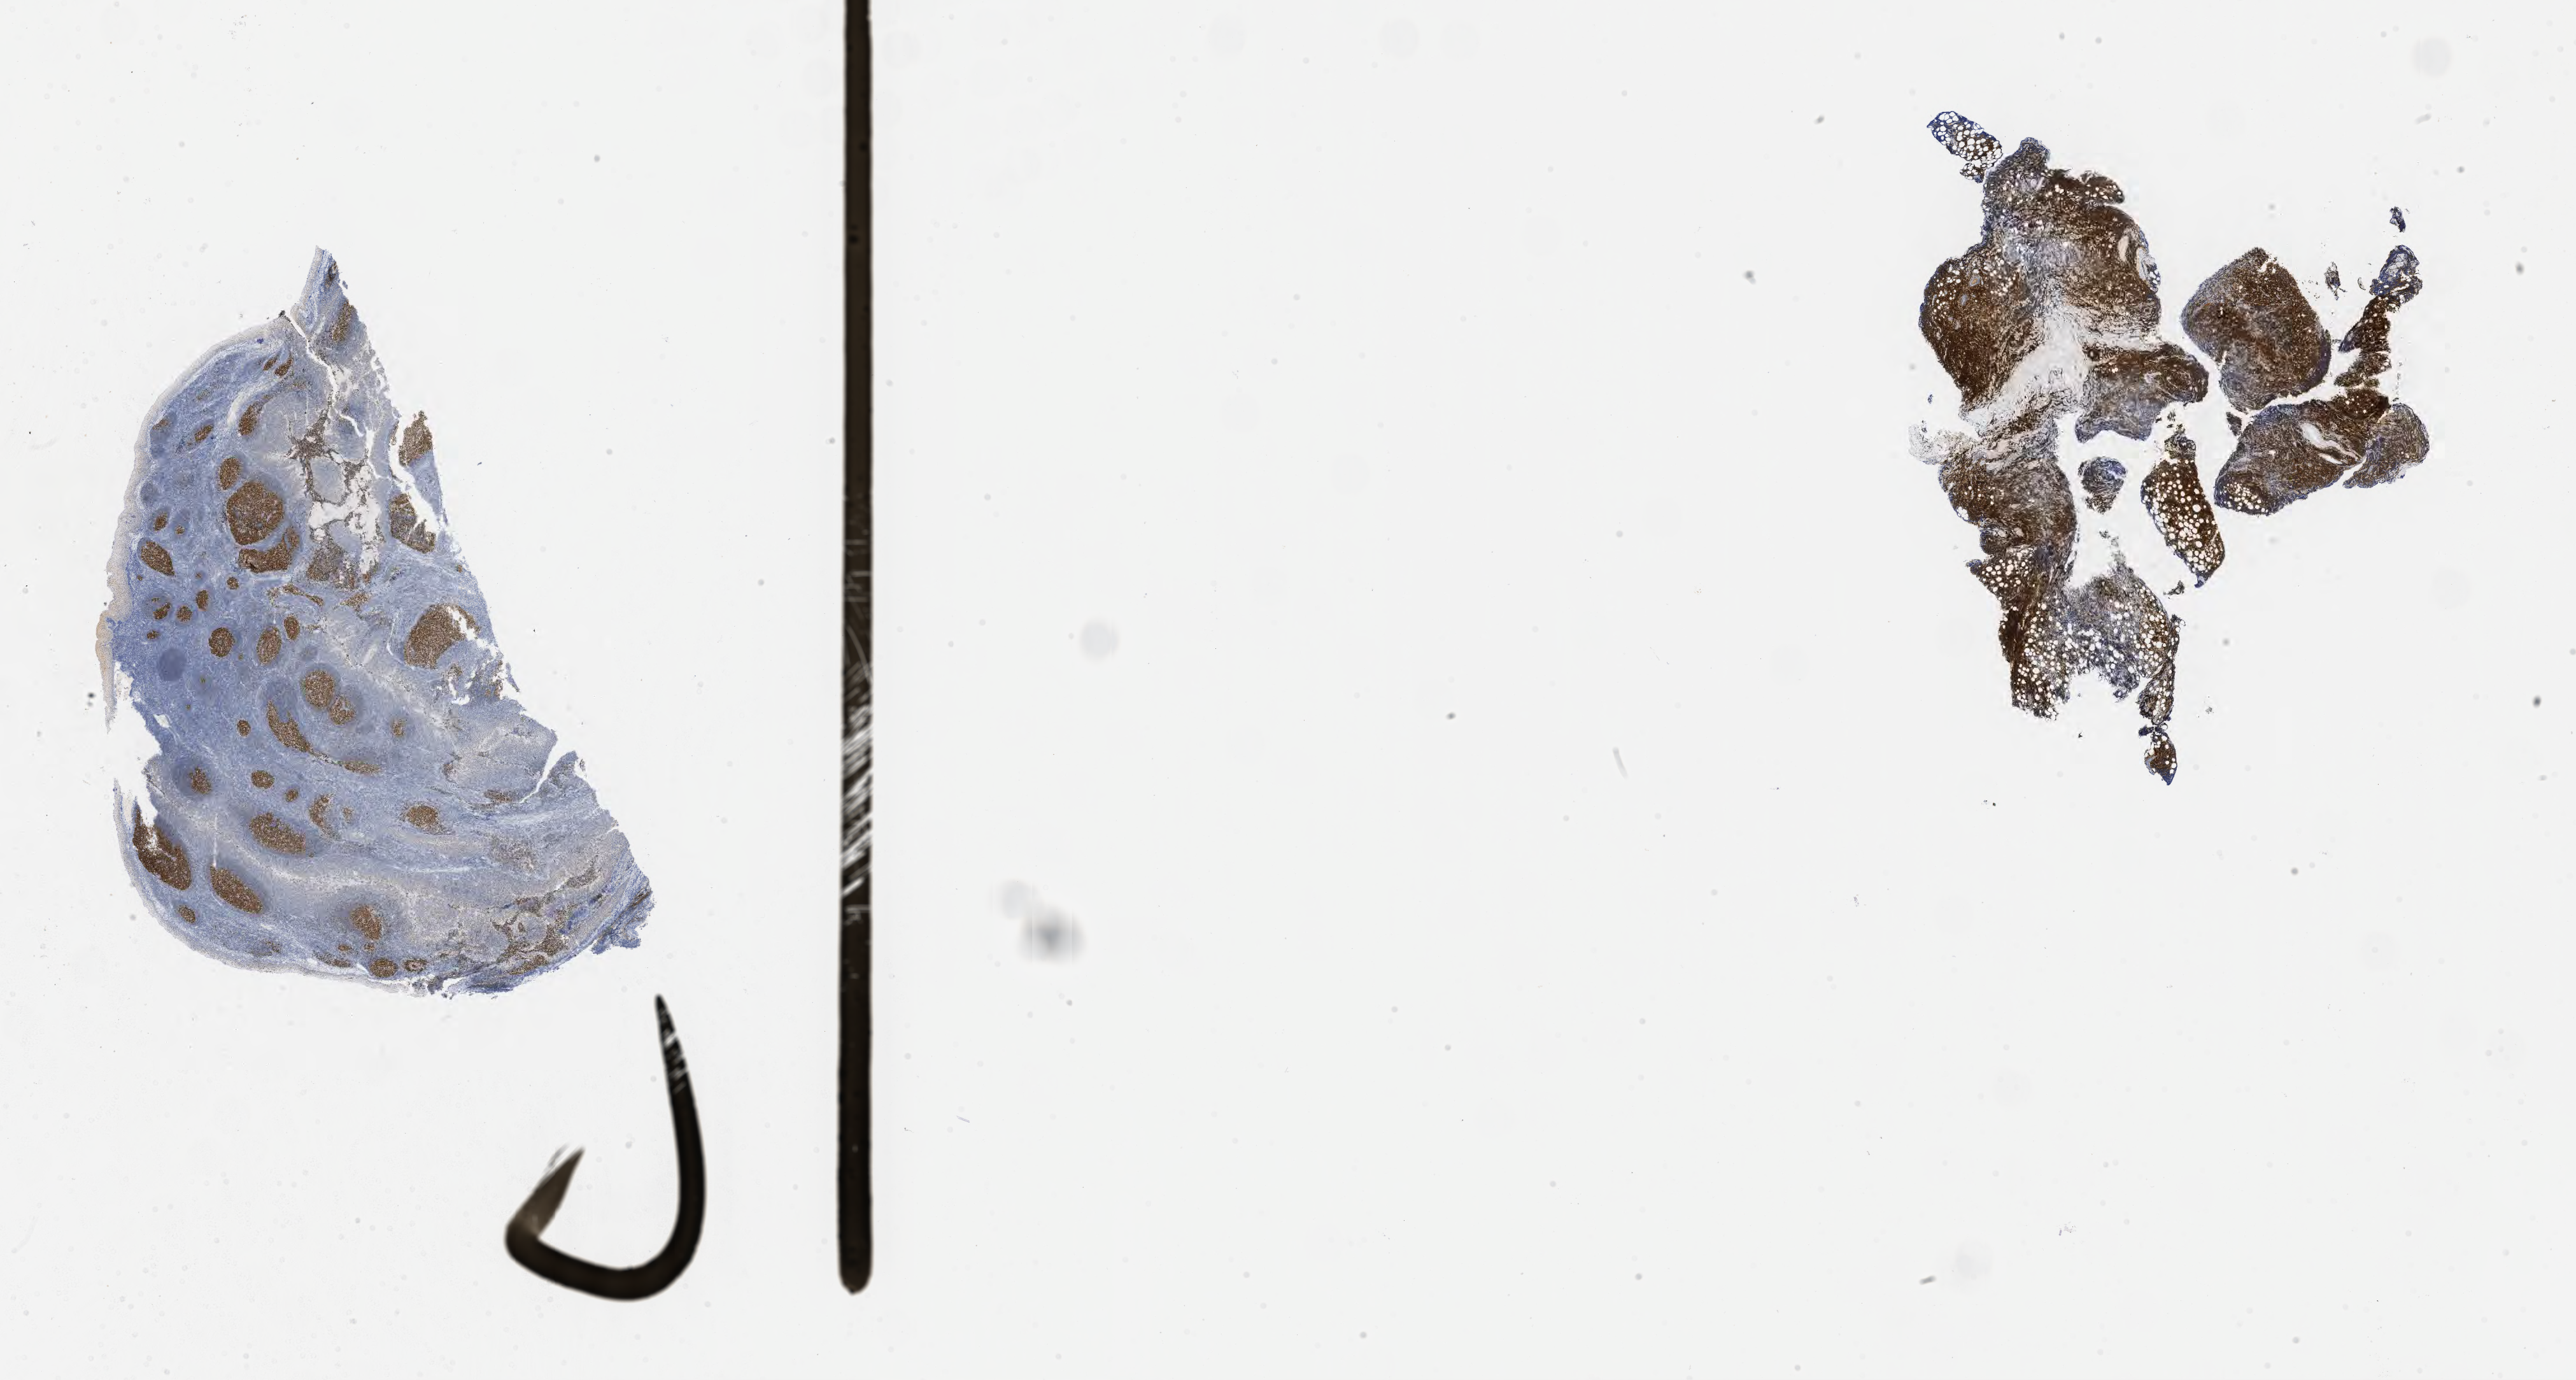
Immunohistochemistry (IHC) whole-slide image stained for BCL6, whole scanned area (about 32.7 x 17.5 mm) shown as a low-resolution overview, specimen: tumor tissue, site: orbit. Male patient, age 20 years.
- diagnosis: Burkitt lymphoma, NOS